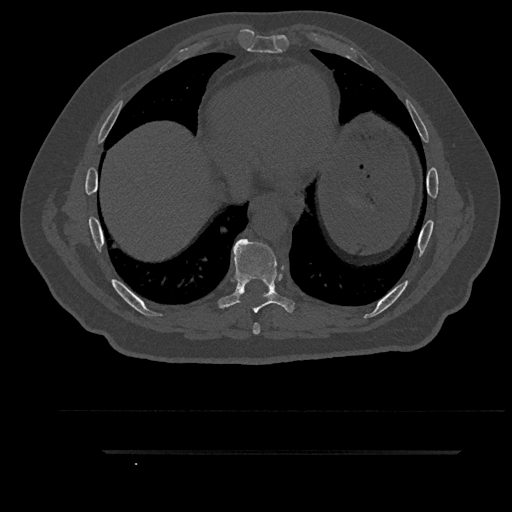
CT including the spine, one axial slice; position 479 of 797 along the scan axis; reconstruction kernel Br40s/3; 120 kVp; bone window (W 1800 / L 400 HU); 0.5 mm slice thickness; 512 × 512 image matrix. Patient: male, 63 years. Case-level facts recorded for this patient, not image findings: primary cancer: renal.
Outlined on this slice (semi-automatic segmentation, software-assisted and operator-edited):
- T7 vertebra: bounding box [x1, y1, x2, y2] px = [253, 323, 260, 335]
- T8 vertebra: [216, 239, 296, 314]